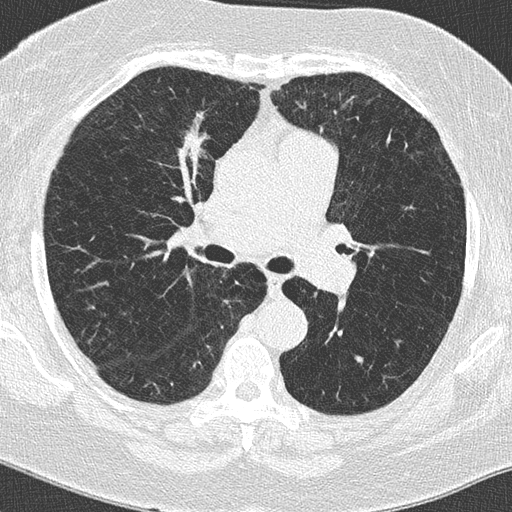
Axial slice from a low-dose chest CT screening exam; second screening round (one year after baseline); lung window (W 1500 / L -600 HU); 2 mm slice thickness; lung (sharp) reconstruction kernel (B50f); 120 kVp; slice 57 of 152 in the series; 512 × 512 image matrix. Female participant, aged 62 years at enrolment.
Expert-annotated lung lesion, bounding box [x1, y1, x2, y2] px = [159, 115, 225, 177]. The screening reader recorded 2 non-calcified nodules or masses ≥4 mm on this exam (left lower lobe, right middle lobe); which of them this box marks is not recorded. Official screen result: positive, other. Later outcome: lung cancer diagnosed 396 days after this screen — adenocarcinoma, NOS, right upper lobe, moderately differentiated (G2), stage IA (AJCC 6th edition), 15 mm at pathology.